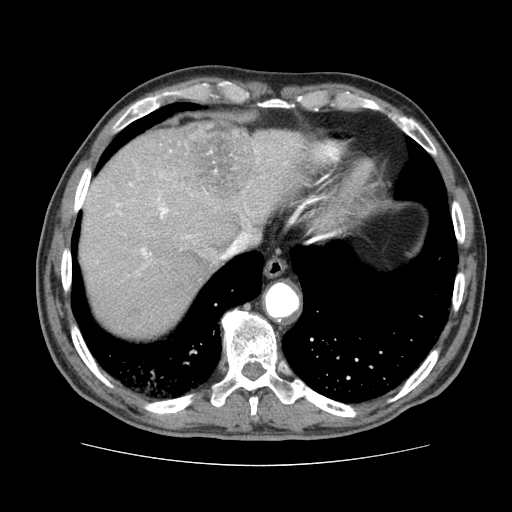
Contrast-enhanced abdominal CT (liver protocol), one axial slice; slice 65 of 79 in the series (ordered by position); reconstruction kernel STANDARD; soft-tissue window (W 400 / L 40 HU); 512 × 512 image matrix. Case-level facts recorded for this patient, not image findings: diagnosis: hepatocellular carcinoma (patient treated with transarterial chemoembolisation; whether this scan precedes or follows treatment is not stated here); TNM stage (as recorded): Stage-I; Child-Pugh class: A.
Outlined on this slice (semi-automatic segmentation, software-assisted and operator-edited):
- liver parenchyma outside the tumour (the mass and vessels are separate outlines, so this box may not span the whole liver): bounding box [x1, y1, x2, y2] px = [80, 124, 306, 336]
- mass: [157, 125, 259, 211]
- liver vessels: [116, 151, 257, 257]